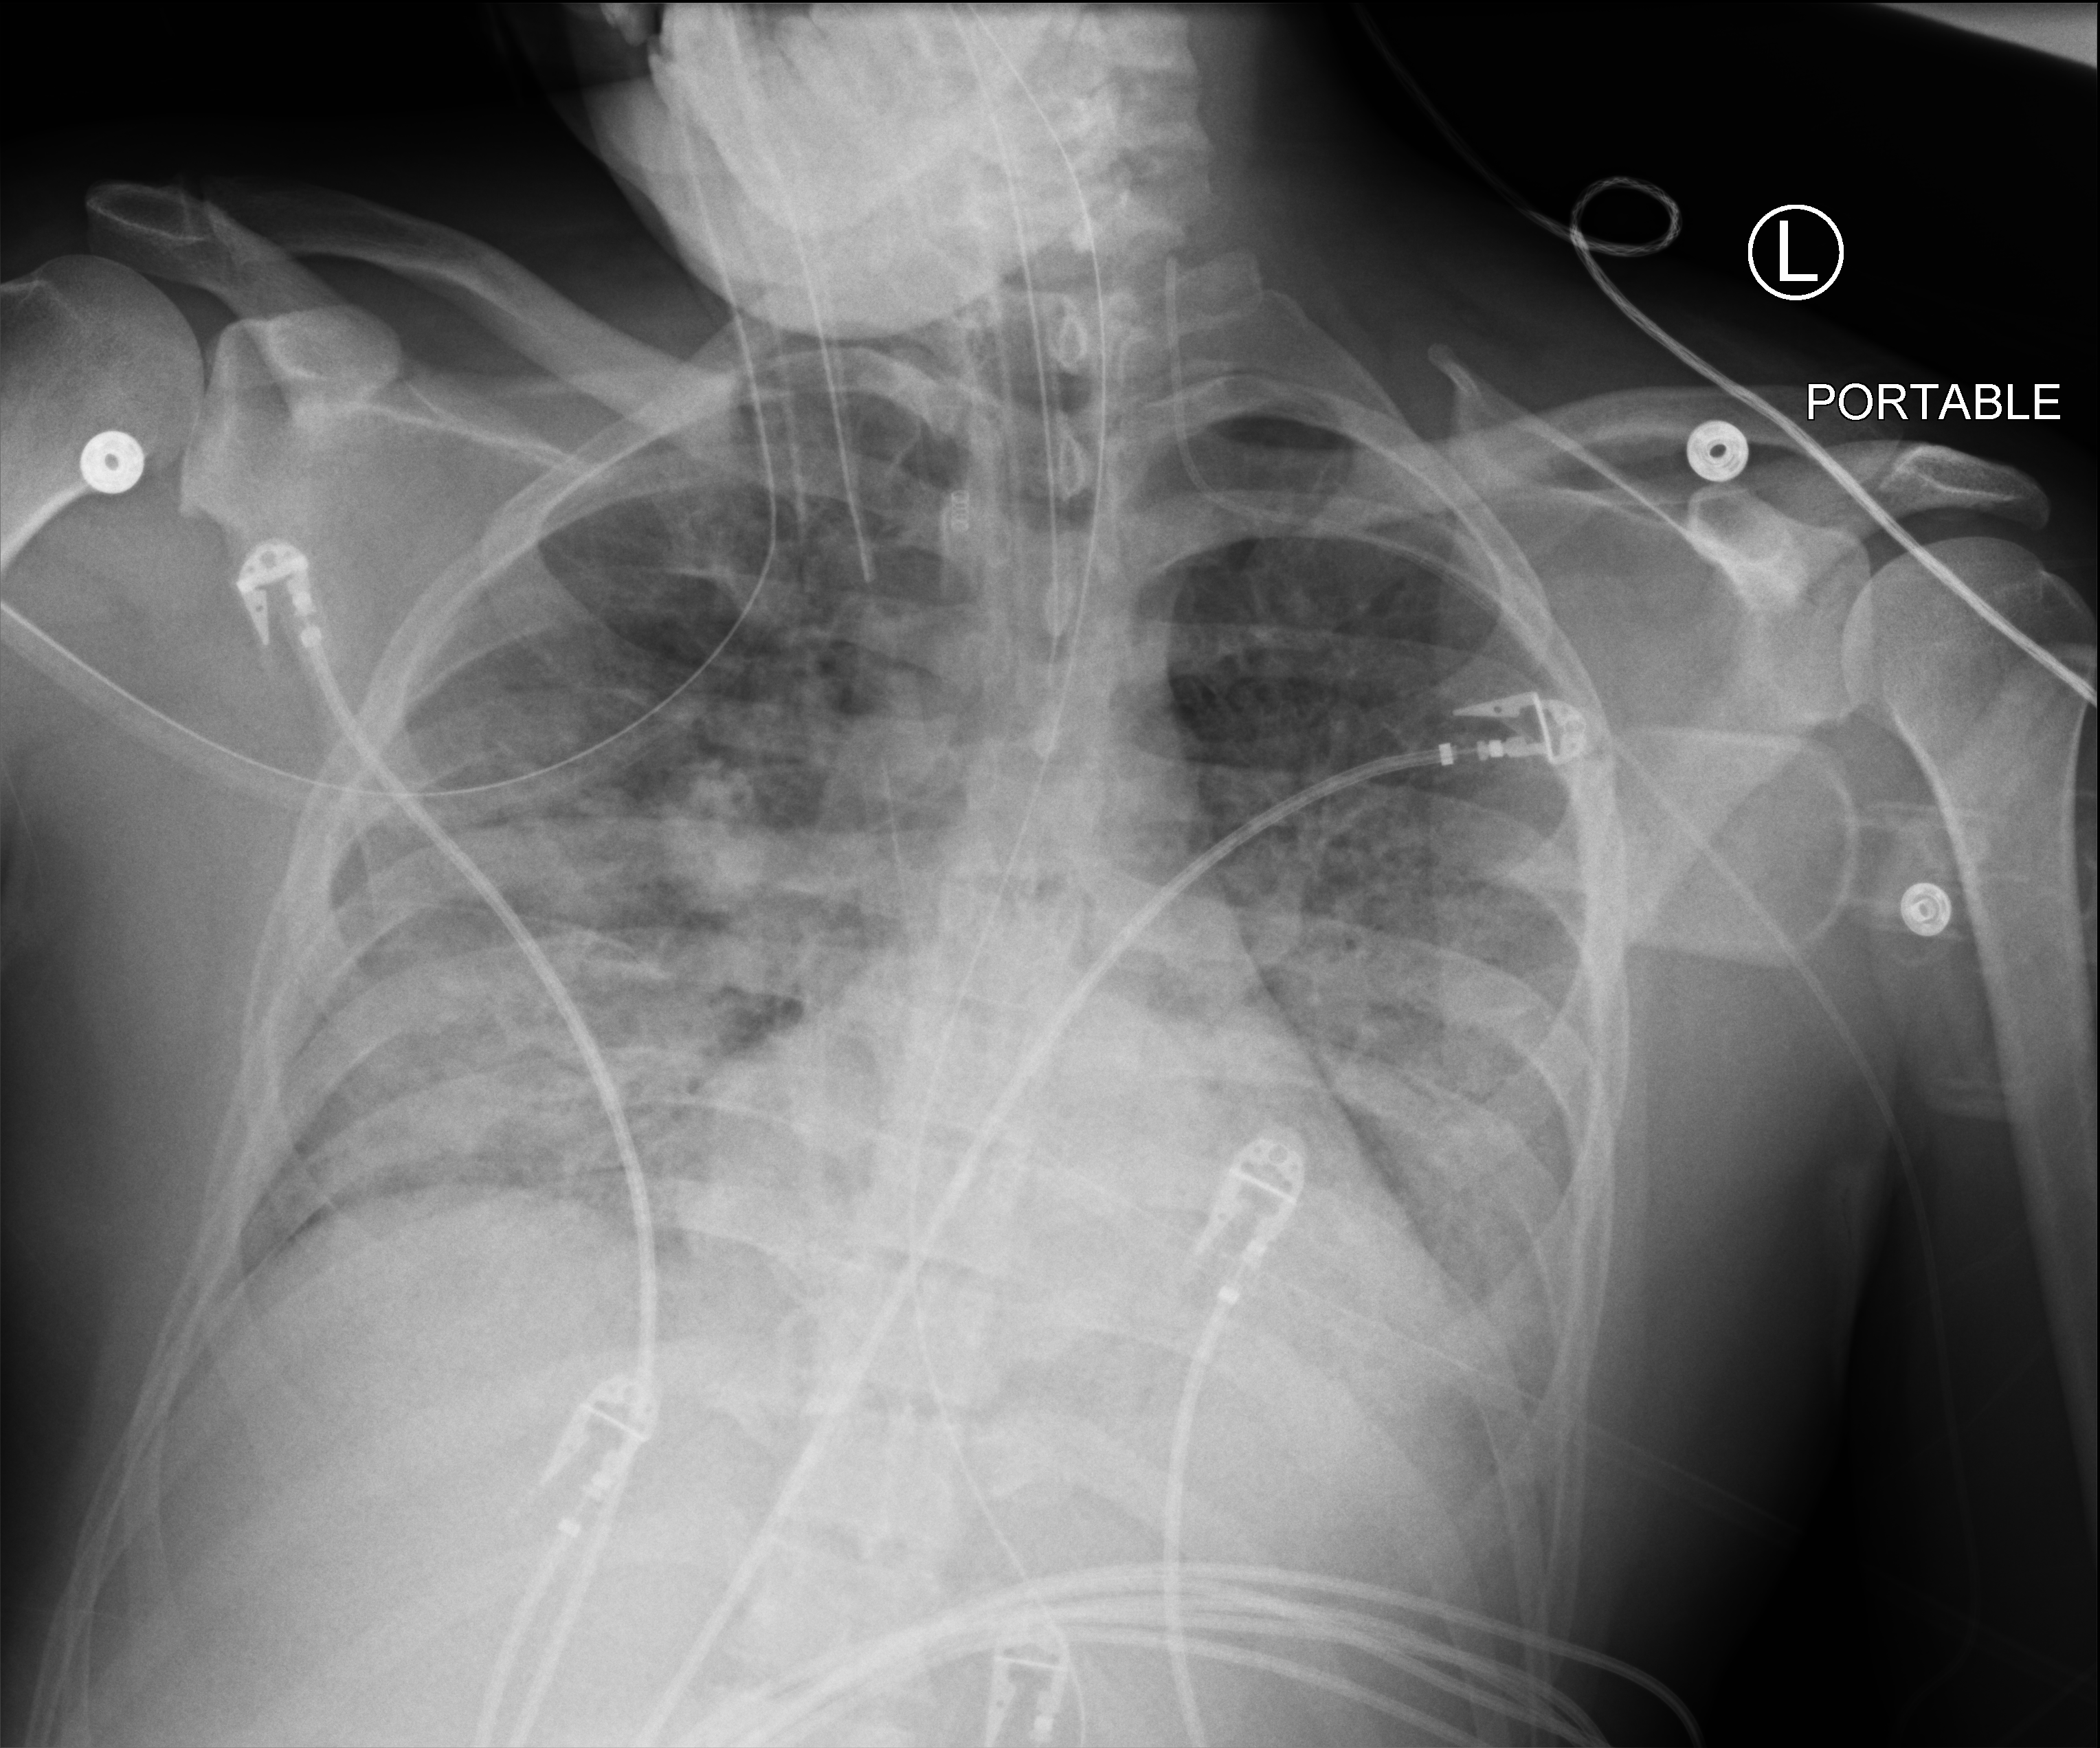
Chest X-ray (portable); anteroposterior (AP) projection. Male patient hospitalised with COVID-19, age 18–59 years.
Admission-level facts for this patient (not findings on this image; timing relative to this image not recorded): other chronic lung disease (admission record): no; mechanically ventilated during this hospital stay: yes; admitted to intensive care during this hospital stay: yes.